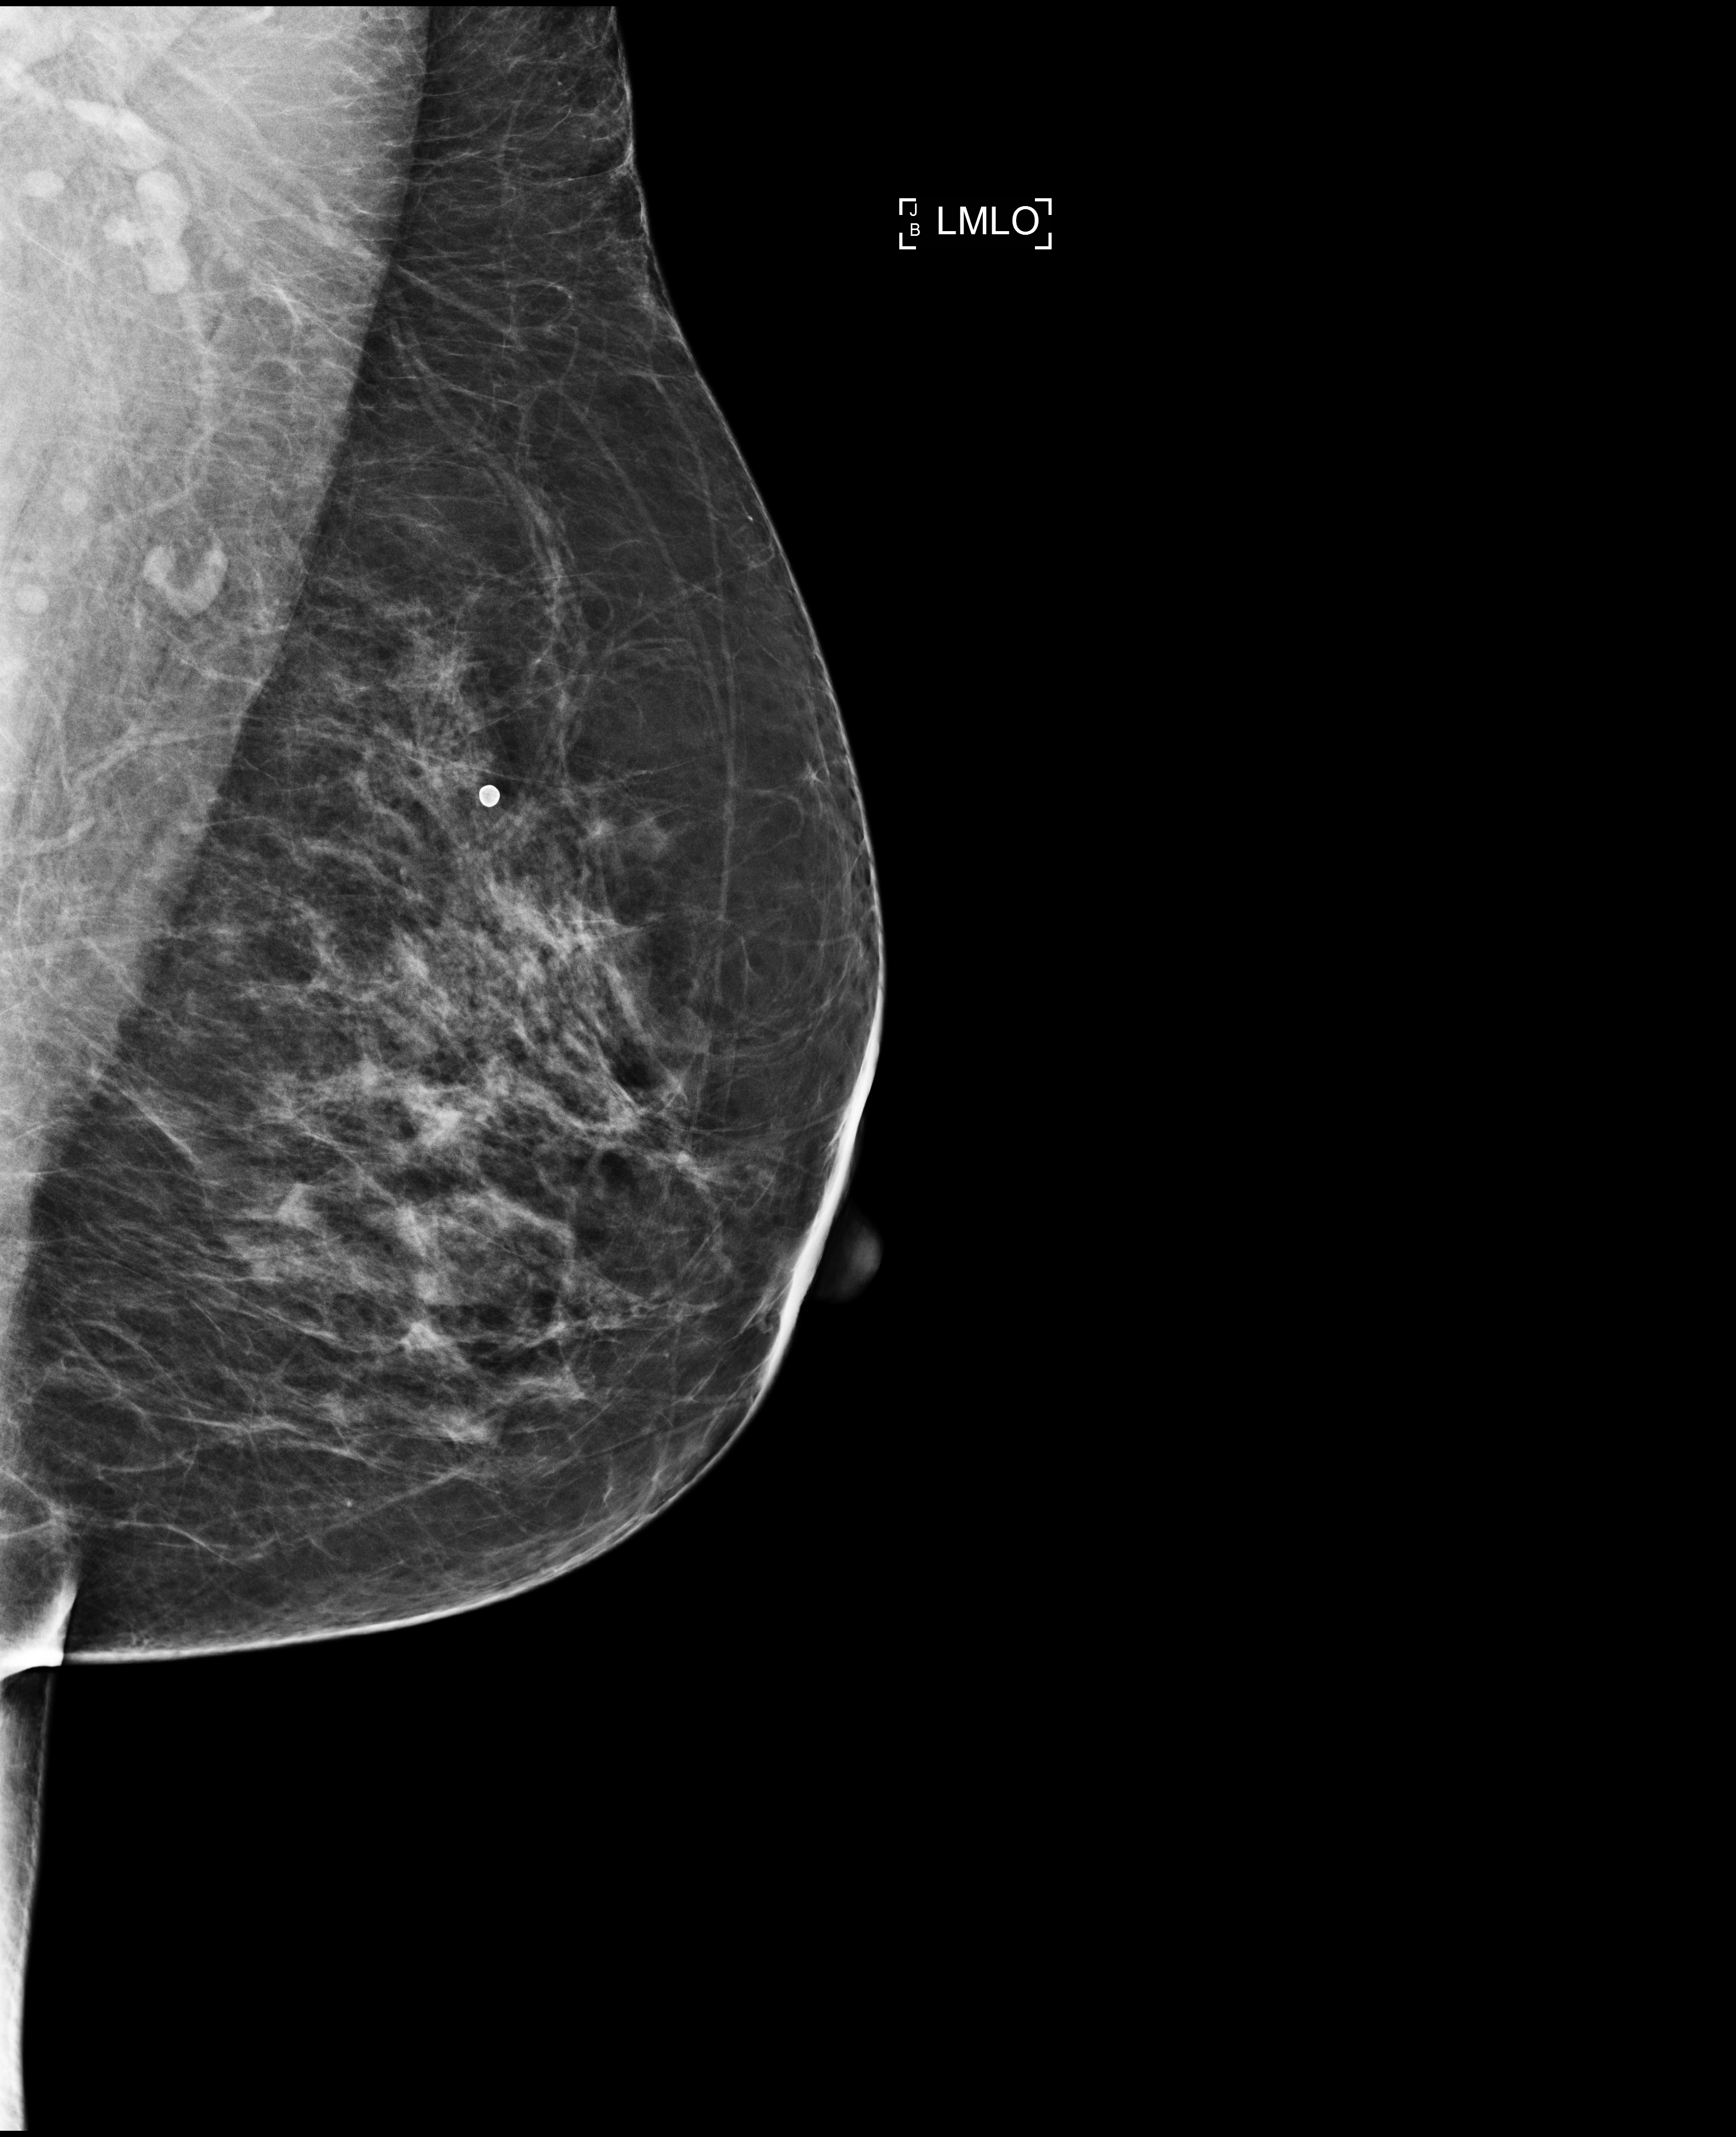
Digital mammogram (FFDM); left breast; MLO view; annual screening mammography examination. Patient aged 63 years (female).
Breast density at the screening exam (both breasts): scattered fibroglandular densities (BI-RADS density category b). Final BI-RADS category for the screening round (tomosynthesis exam, both breasts): category 1. Recall: no recall after this screen.